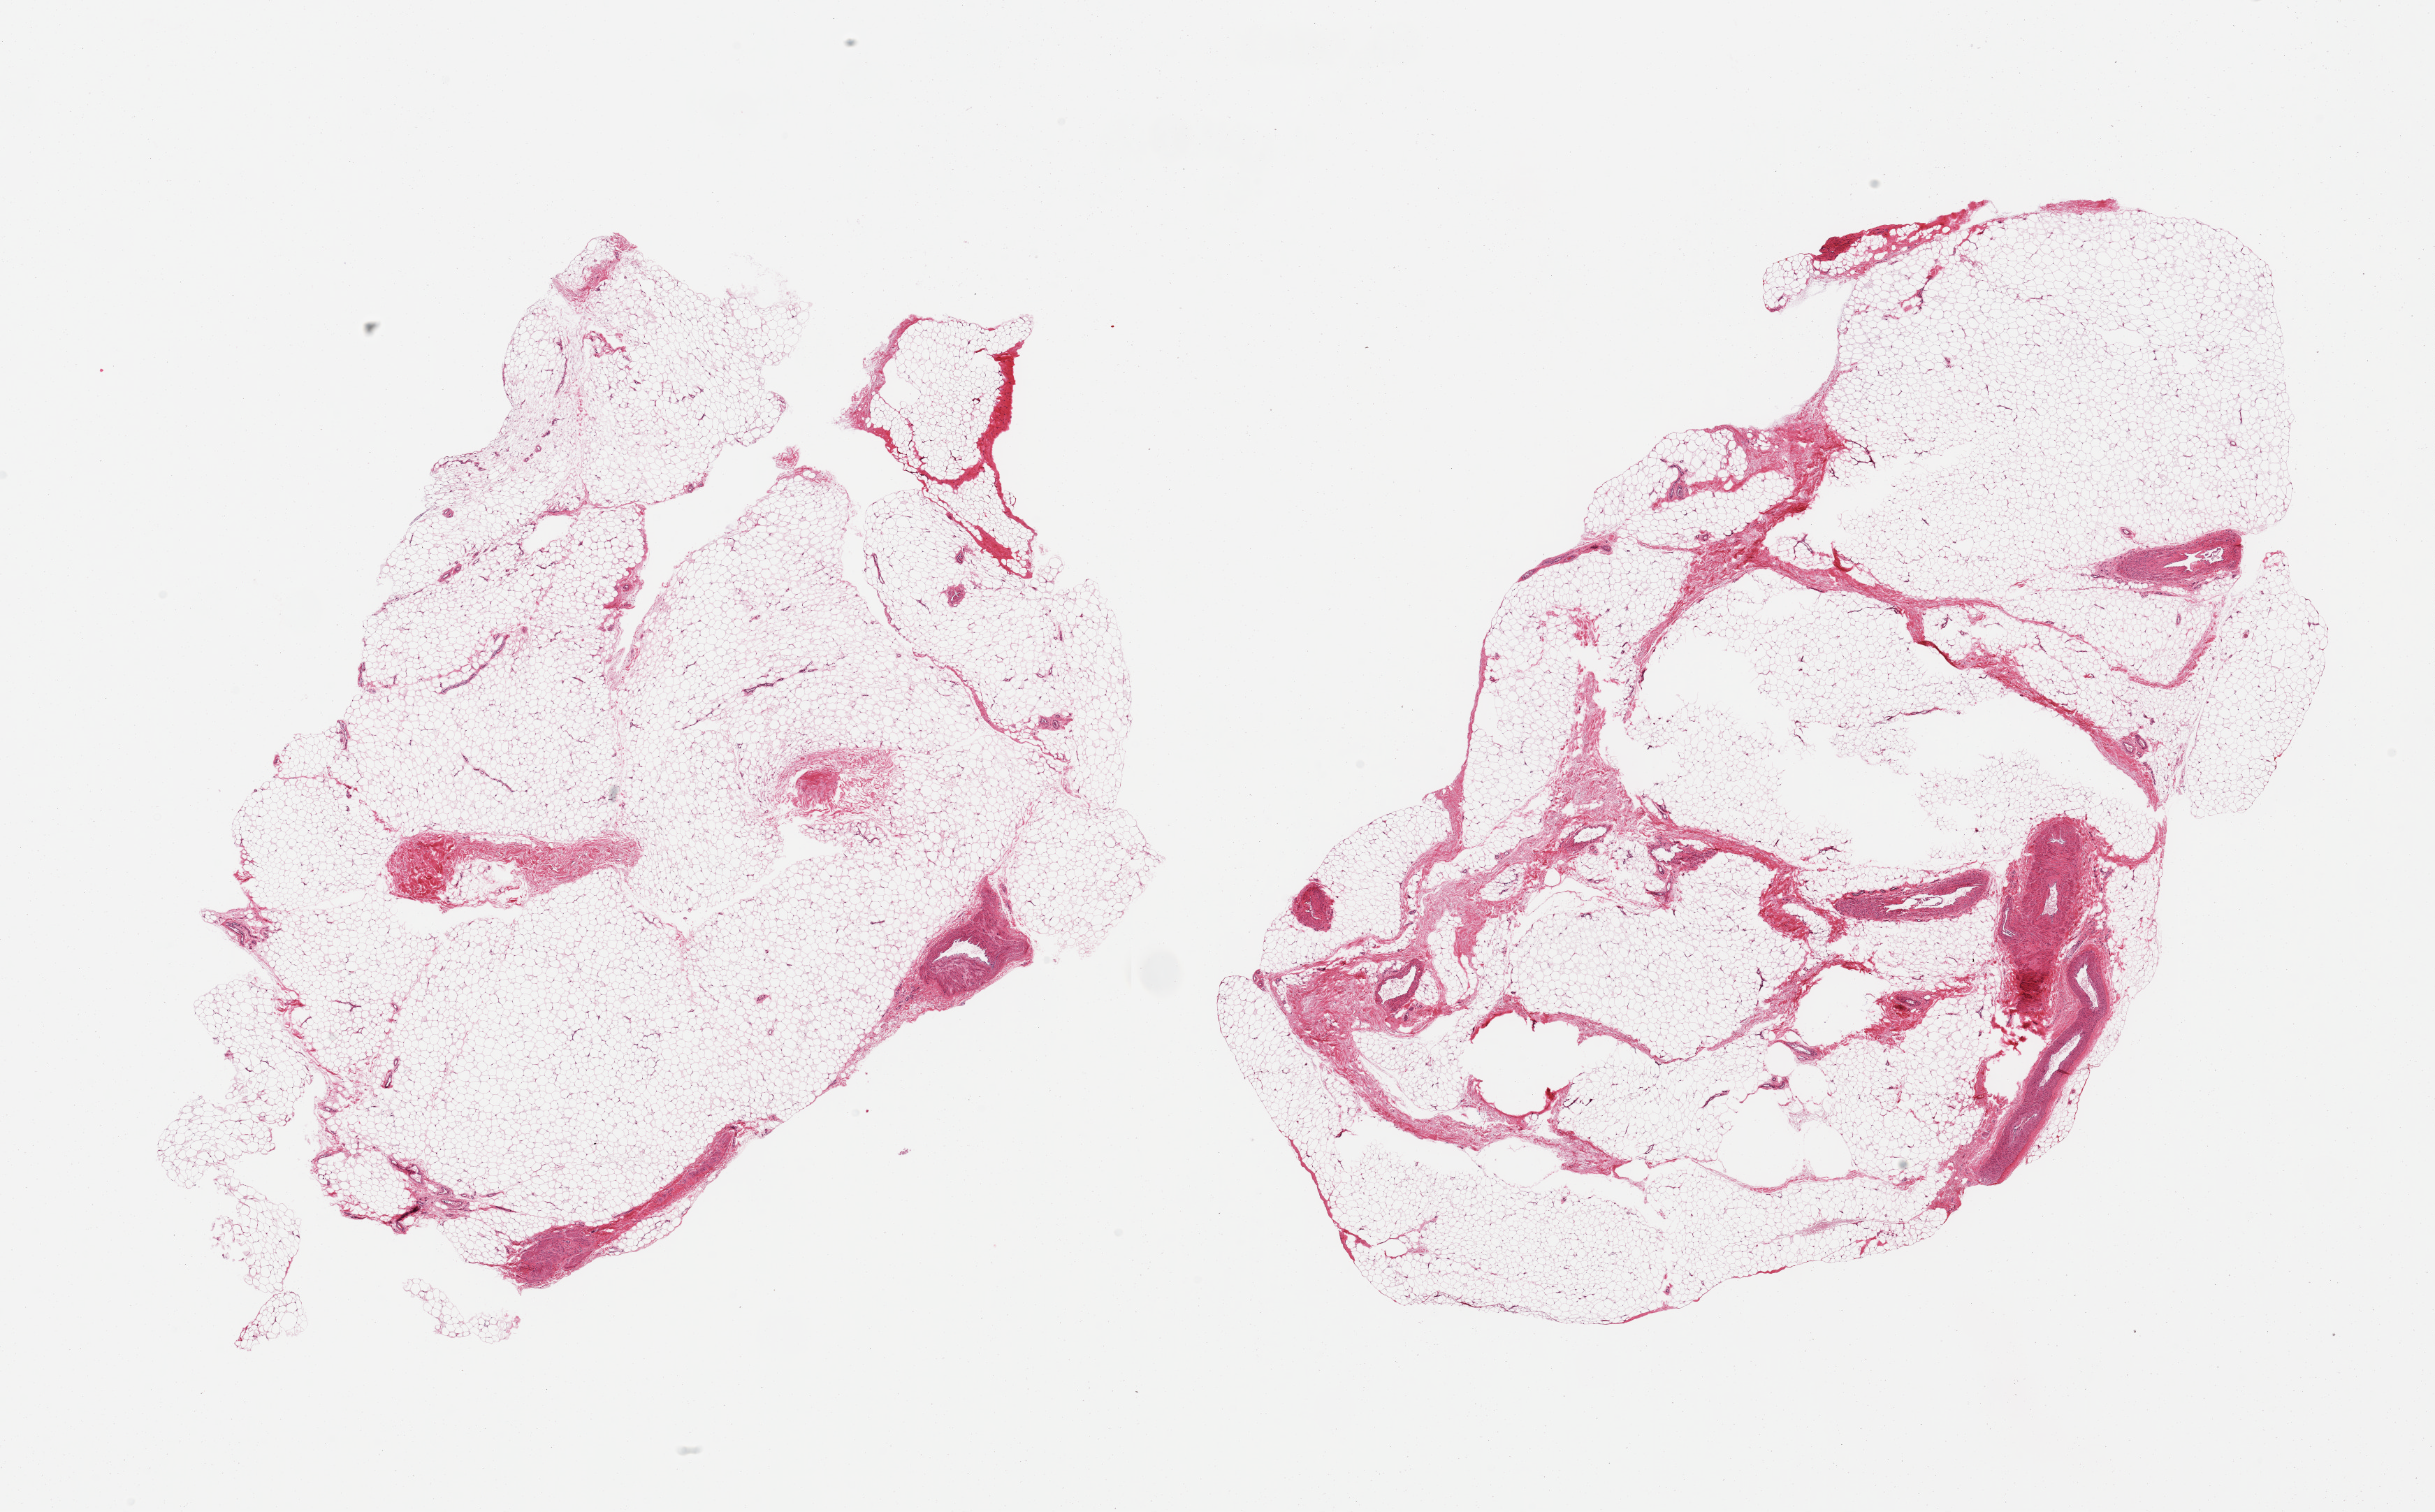
Whole-slide image, hematoxylin and eosin (H&E) stain, a low-resolution overview of the entire scanned area, about 27.6 x 17.1 mm (acquisition: 20x scan). PAXgene-fixed, paraffin-embedded tissue. Section of adipose tissue (target tissue). Donor tissue sample. Donor: male.
* reviewer comment on this tissue sample: 2 pieces; 5% vascular content